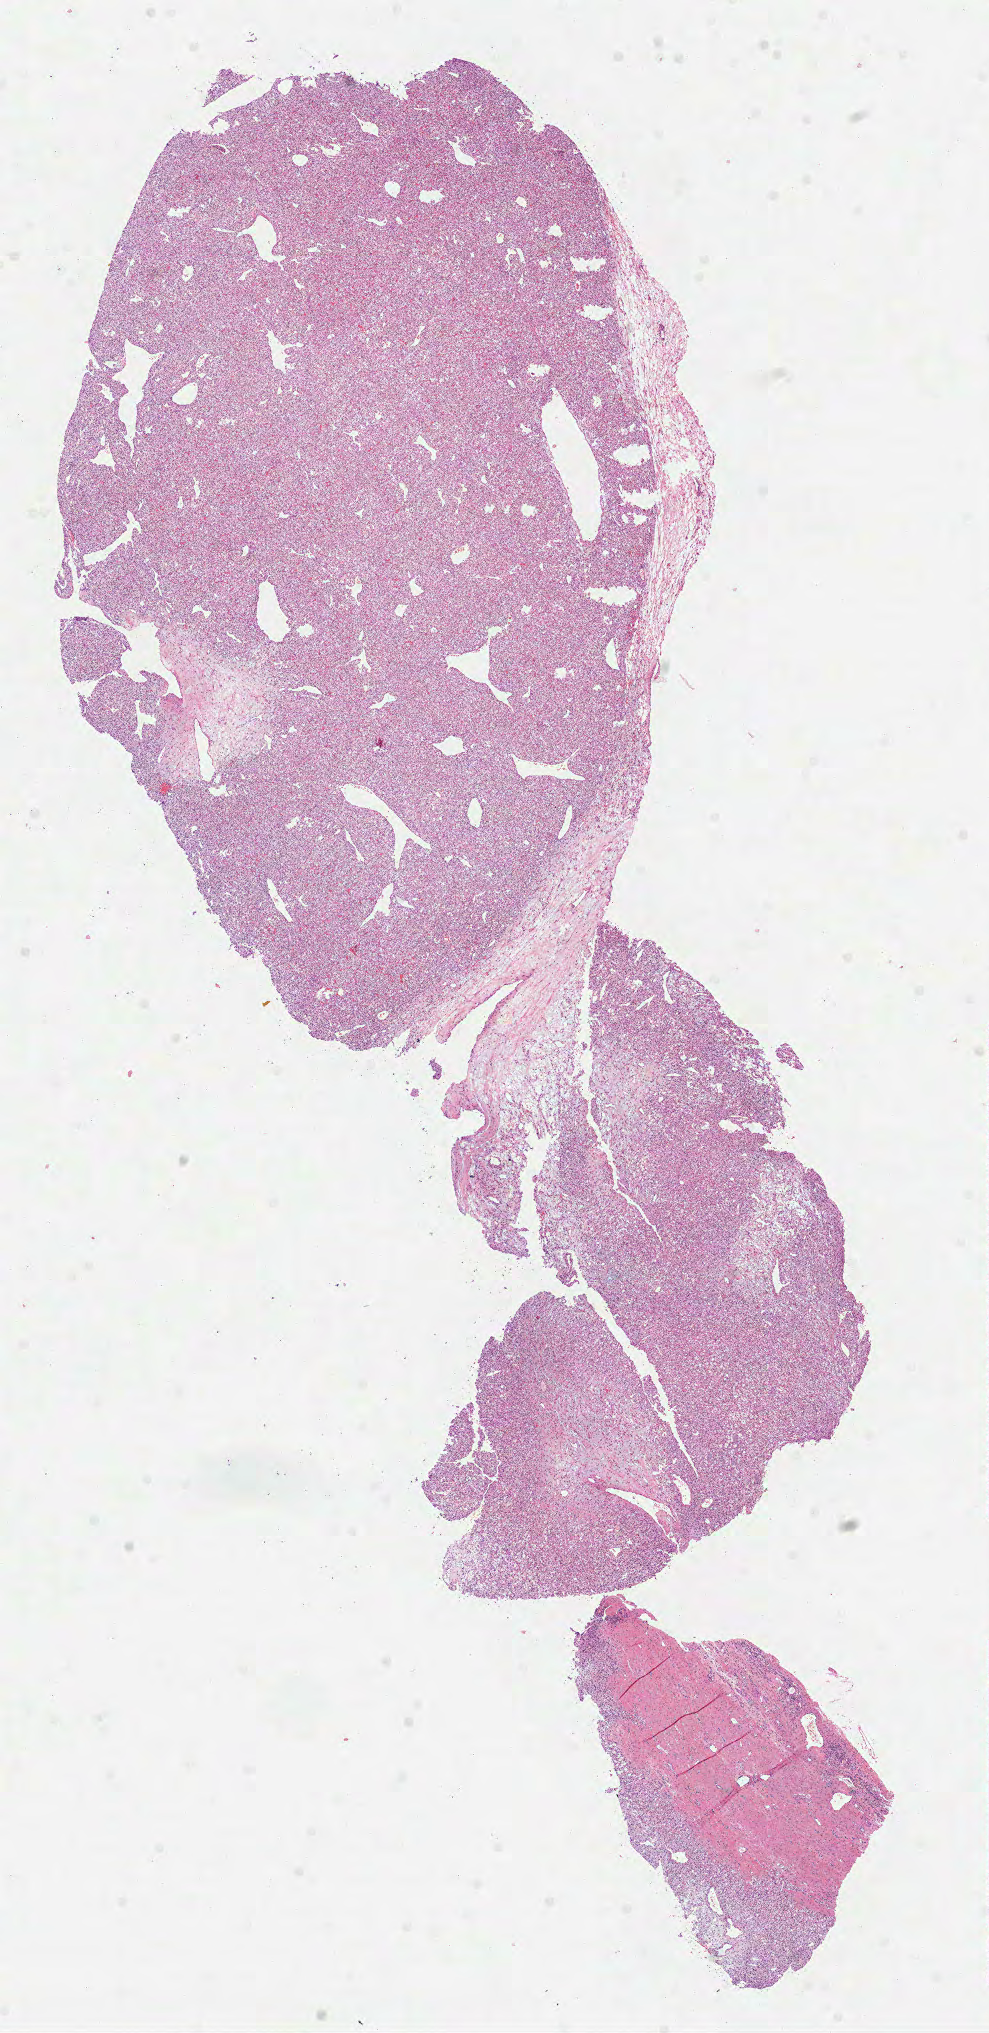
Hematoxylin and eosin (H&E) stained whole-slide image, low-resolution overview of the scanned area, about 8.0 x 16.4 mm (acquisition: 40x scan). Formalin-fixed paraffin-embedded (FFPE) diagnostic section. Primary tumour sample from the kidney. Male, age 72 years at initial diagnosis. Histologic grade: G3 (poorly differentiated).
TNM: T1b N0 M0. Pathologic diagnosis: Clear cell adenocarcinoma, NOS. AJCC pathologic stage: I.